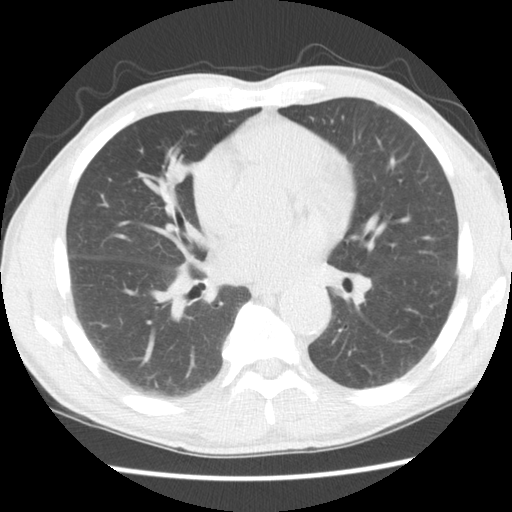
Low-dose screening chest CT, axial slice. Second annual screen. Lung window (W 1500 / L -600 HU). 2.5 mm slice thickness. Slice 79 of 152 in the series. Male, age 65 years at enrolment. Current smoker at enrolment.
- Lesion marked by an expert reader, bounding box <131,147,200,214> (left, top, right, bottom; pixels).
- Screening reader's record for this exam (one nodule recorded; not confirmed to be the boxed lesion): non-calcified nodule or mass ≥4 mm, right middle lobe, 11 × 9 mm, smooth margins, soft tissue attenuation, pre-existing on the prior screen: no.
- Official screen result: positive, other.
- Participant outcome: lung cancer diagnosed 601 days after this screen (after the third annual screen) — squamous cell carcinoma, NOS, right middle lobe, poorly differentiated (G3), stage IA (AJCC 6th edition), 23 mm at pathology.